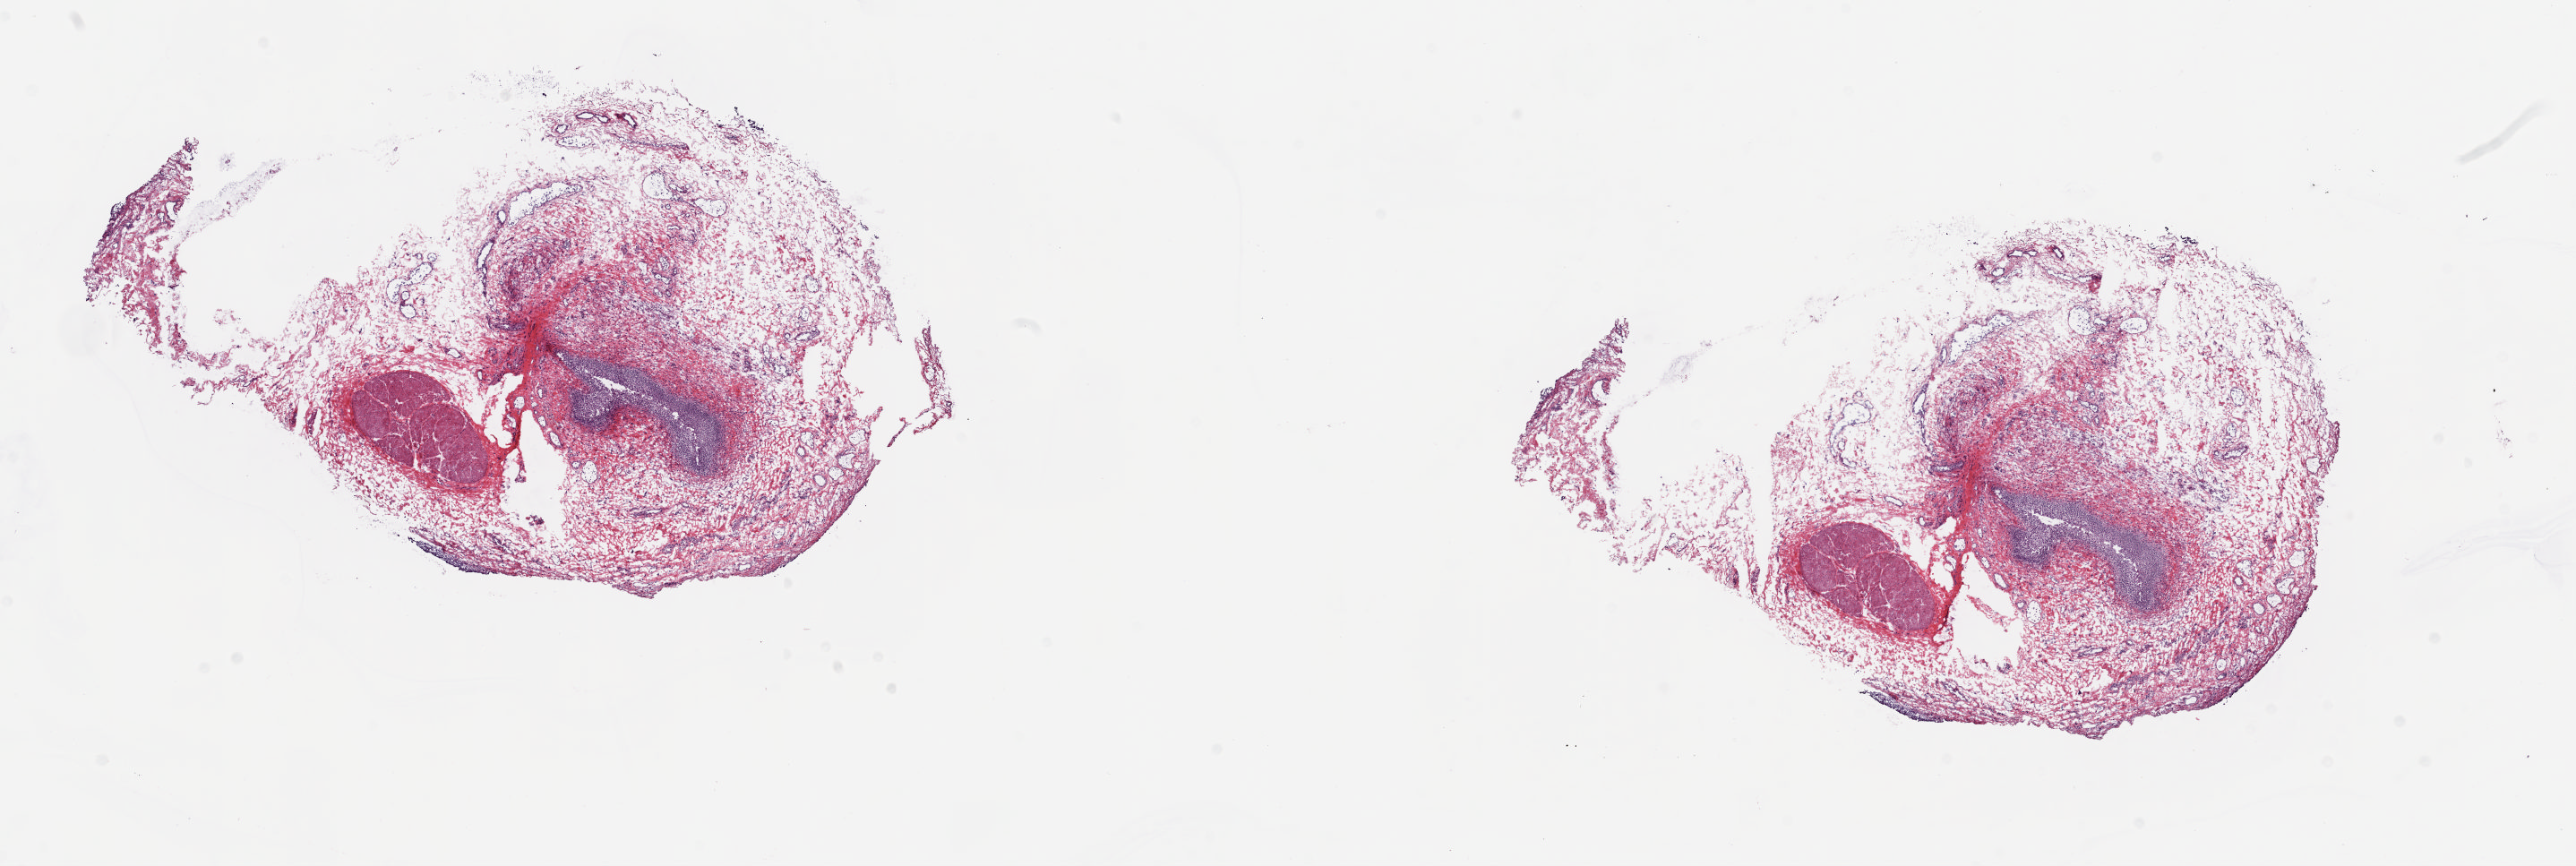
Digitized H&E tissue section (whole slide) — low-resolution overview of the scanned area, about 22.8 x 7.7 mm (acquisition: 20x scan); frozen section; solid tissue normal (non-tumour tissue) sample from the bladder. Patient: male, age at initial diagnosis 59 years. Pathologist review of this section (percent, as recorded): tumour cells 0%, tumour nuclei 0%, normal cells 25%, stromal cells 75%, necrosis 0%. Inflammatory infiltration, as recorded: lymphocyte infiltration 3%, monocyte infiltration 1%, neutrophil infiltration 1%.
This section: solid tissue normal sample (biorepository sample class). Patient diagnosis: Transitional cell carcinoma.